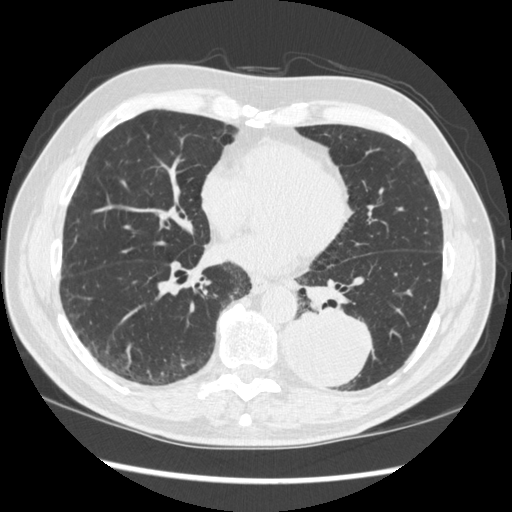
Chest CT (low-dose screening protocol), one axial image. Baseline screening round. Lung window (W 1500 / L -600 HU). Male participant, aged 72 years at enrolment. Current smoker at enrolment.
• Lesion marked by an expert reader, bounding box (x1, y1, x2, y2) in pixels: (270, 300, 374, 390).
• The screening reader recorded 2 non-calcified nodules or masses ≥4 mm on this exam; which of them this box marks is not recorded.
• Official screen result: positive, change unspecified: nodule(s) >= 4 mm or enlarging nodule(s), mass(es), or other non-specific abnormalities suspicious for lung cancer.
• Participant outcome: lung cancer diagnosed 37 days after this screen — squamous cell carcinoma, NOS, left lower lobe, stage IIIA (AJCC 6th edition), 60 mm at pathology.